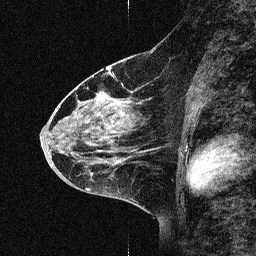
Breast MRI (dynamic contrast-enhanced), one sagittal slice; position 31 of 64 along the scan axis; dynamic contrast-enhanced study with each time point stored as its own series, time point 2 of 3 at this slice position (early post-contrast, ordered by acquisition time); 1.5 T; TE 4.5 ms, TR 11 ms; 2.06 mm slice thickness; 256 × 256 image matrix. Female patient, age 46 years. Case-level facts recorded for this patient, not image findings: setting: breast cancer imaged before/during neoadjuvant chemotherapy; receptor status: HER2-positive.
Structures marked on this image (semi-automatic segmentation, software-assisted and operator-edited):
- analysis volume of interest (the breast-tissue region the enhancement analysis was run in; not a lesion): bounding box <46,51,180,169> (left, top, right, bottom; pixels)
- tumour enhancement mask (voxels above the 90 % enhancement threshold inside the analysis volume of interest): <108,70,139,89>